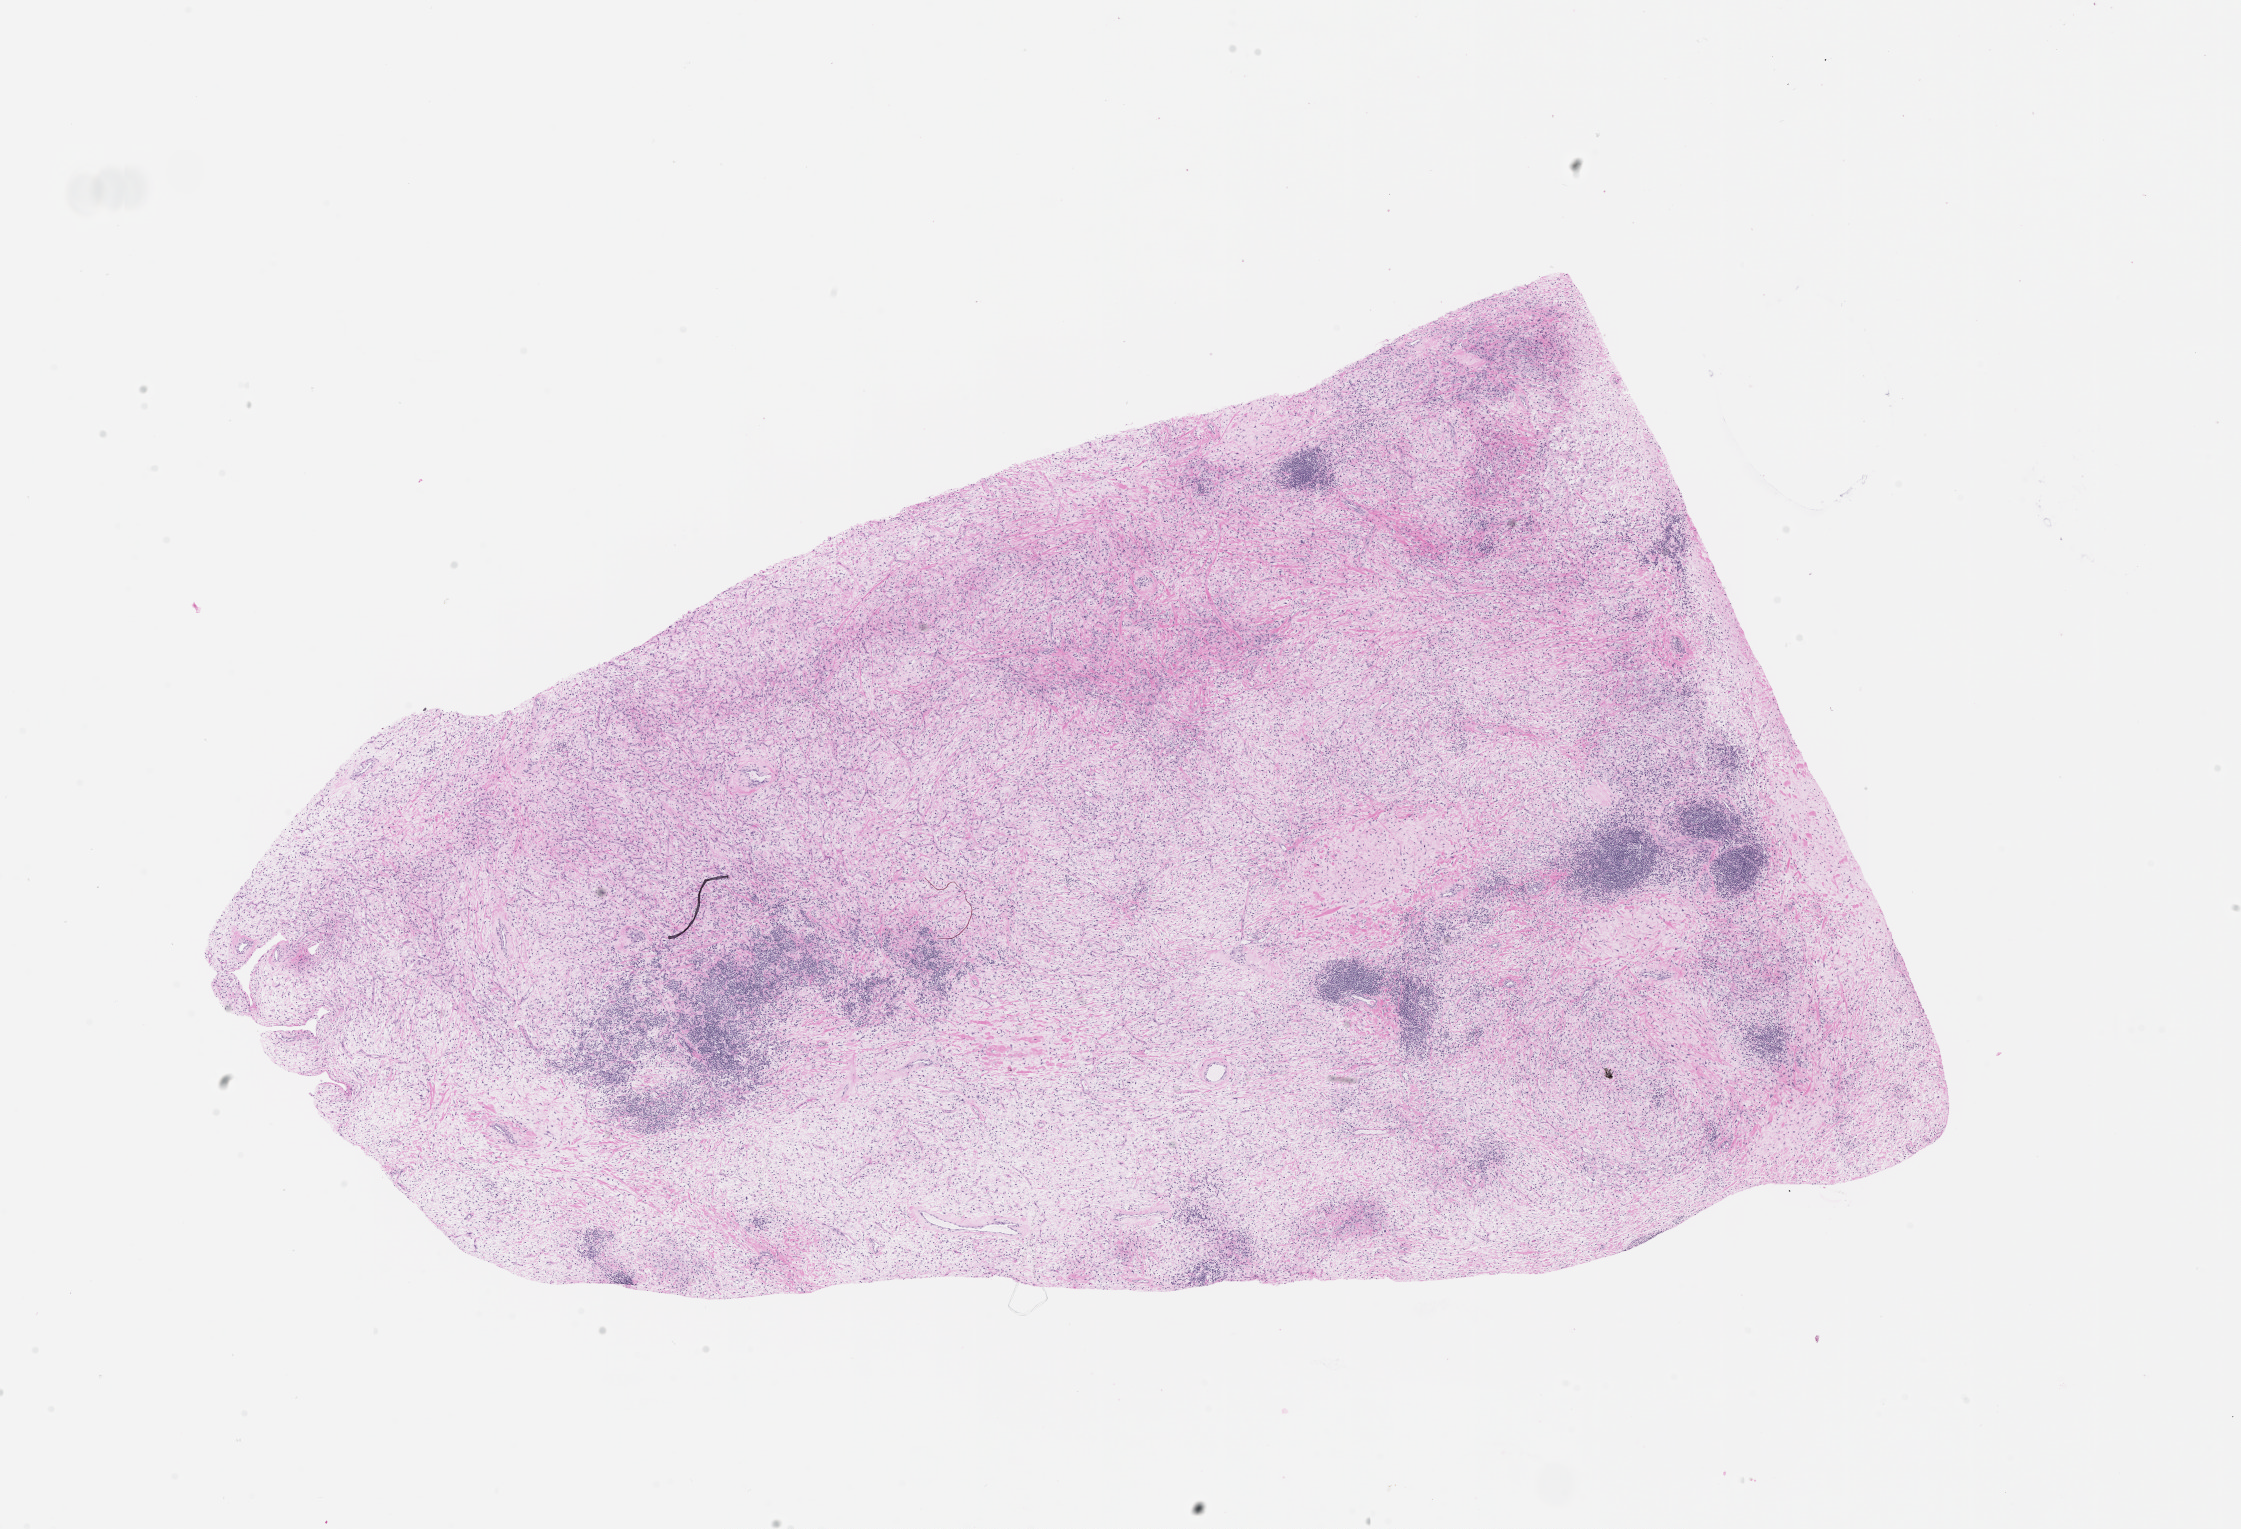
Hematoxylin and eosin (H&E) stained whole-slide image — low-resolution overview of the scanned area, about 18.0 x 12.3 mm.
Patient diagnosis (cohort enrolment): sarcoma (site not recorded at cohort level).